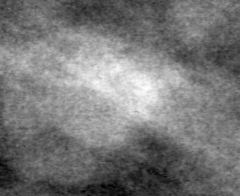
Region of interest cut from a scanned film mammogram (one marked finding); right breast; MLO view; BI-RADS breast density category 2 (scale 1–4).
- Mass, shape round, margins circumscribed; BI-RADS assessment category 3; subtlety rating 3 on a 1 (subtle) to 5 (obvious) scale; pathology (as recorded): benign.